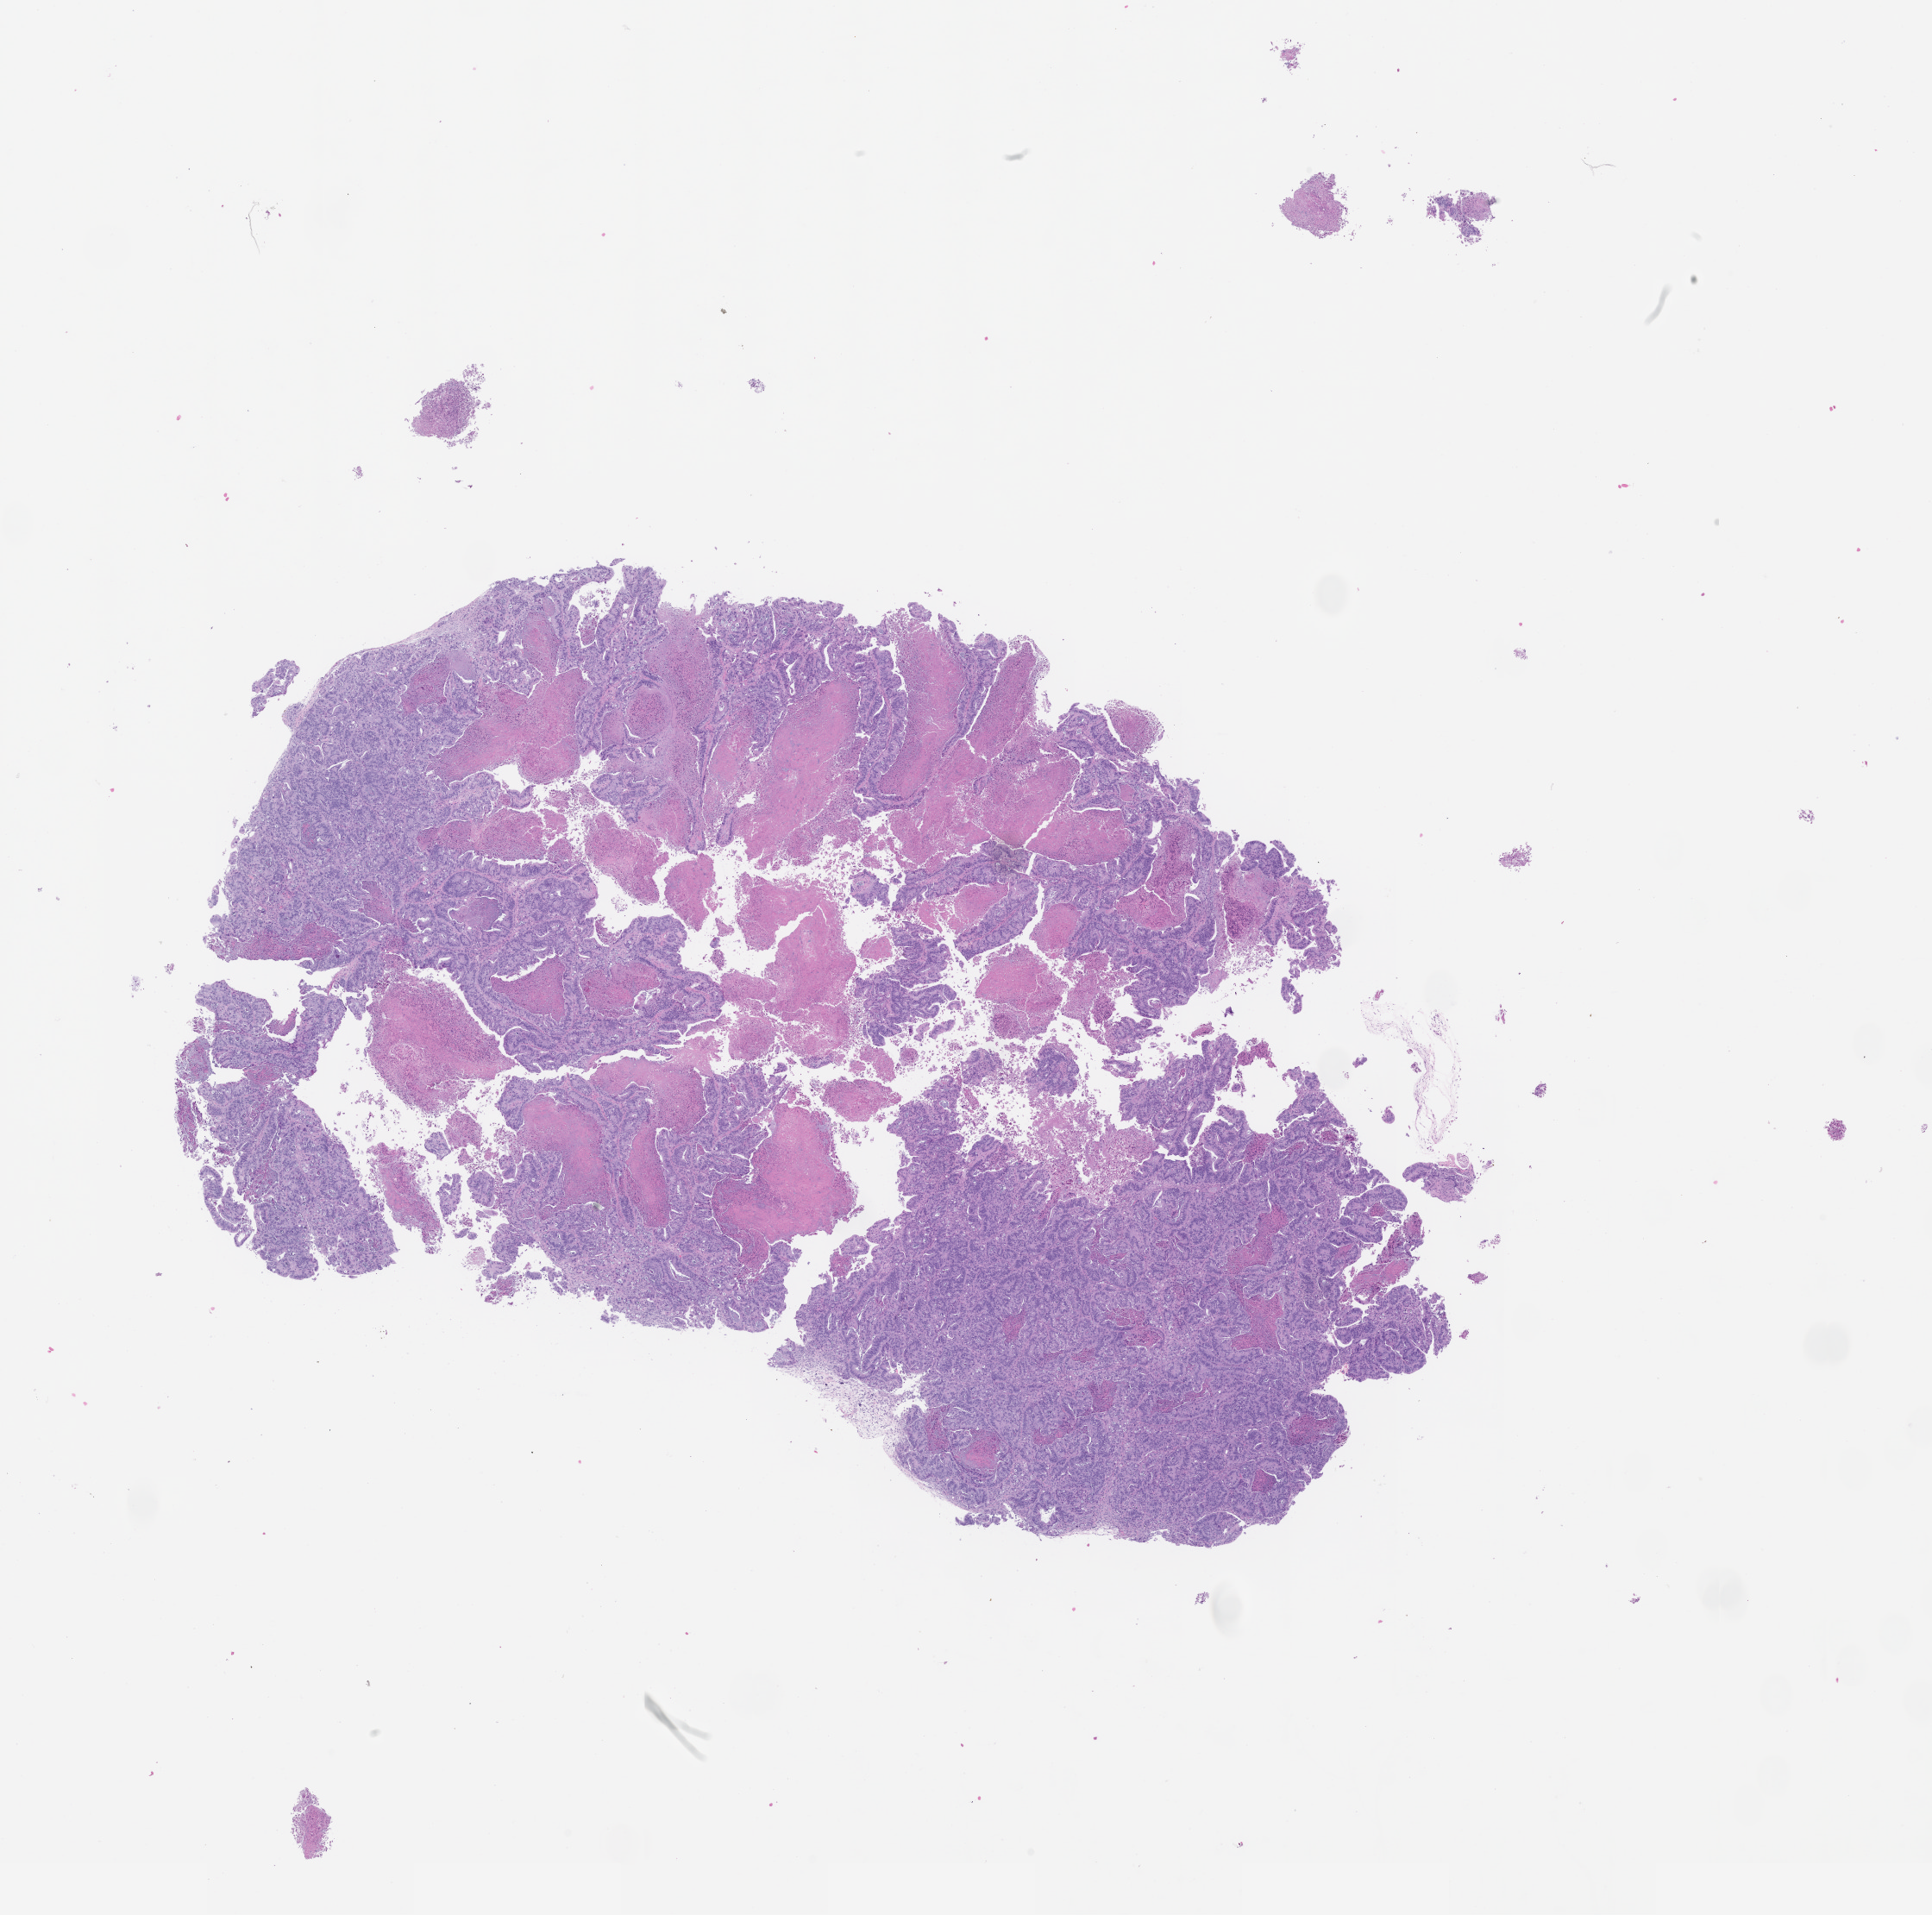
H&E whole-slide image of a patient-derived xenograft (PDX) tumor grown in a mouse, passage 0 — low-resolution overview of the scanned area, about 17.9 x 17.8 mm; FFPE section; originating tumor site category: colon.
Originating patient diagnosis: Colon Adenocarcinoma.